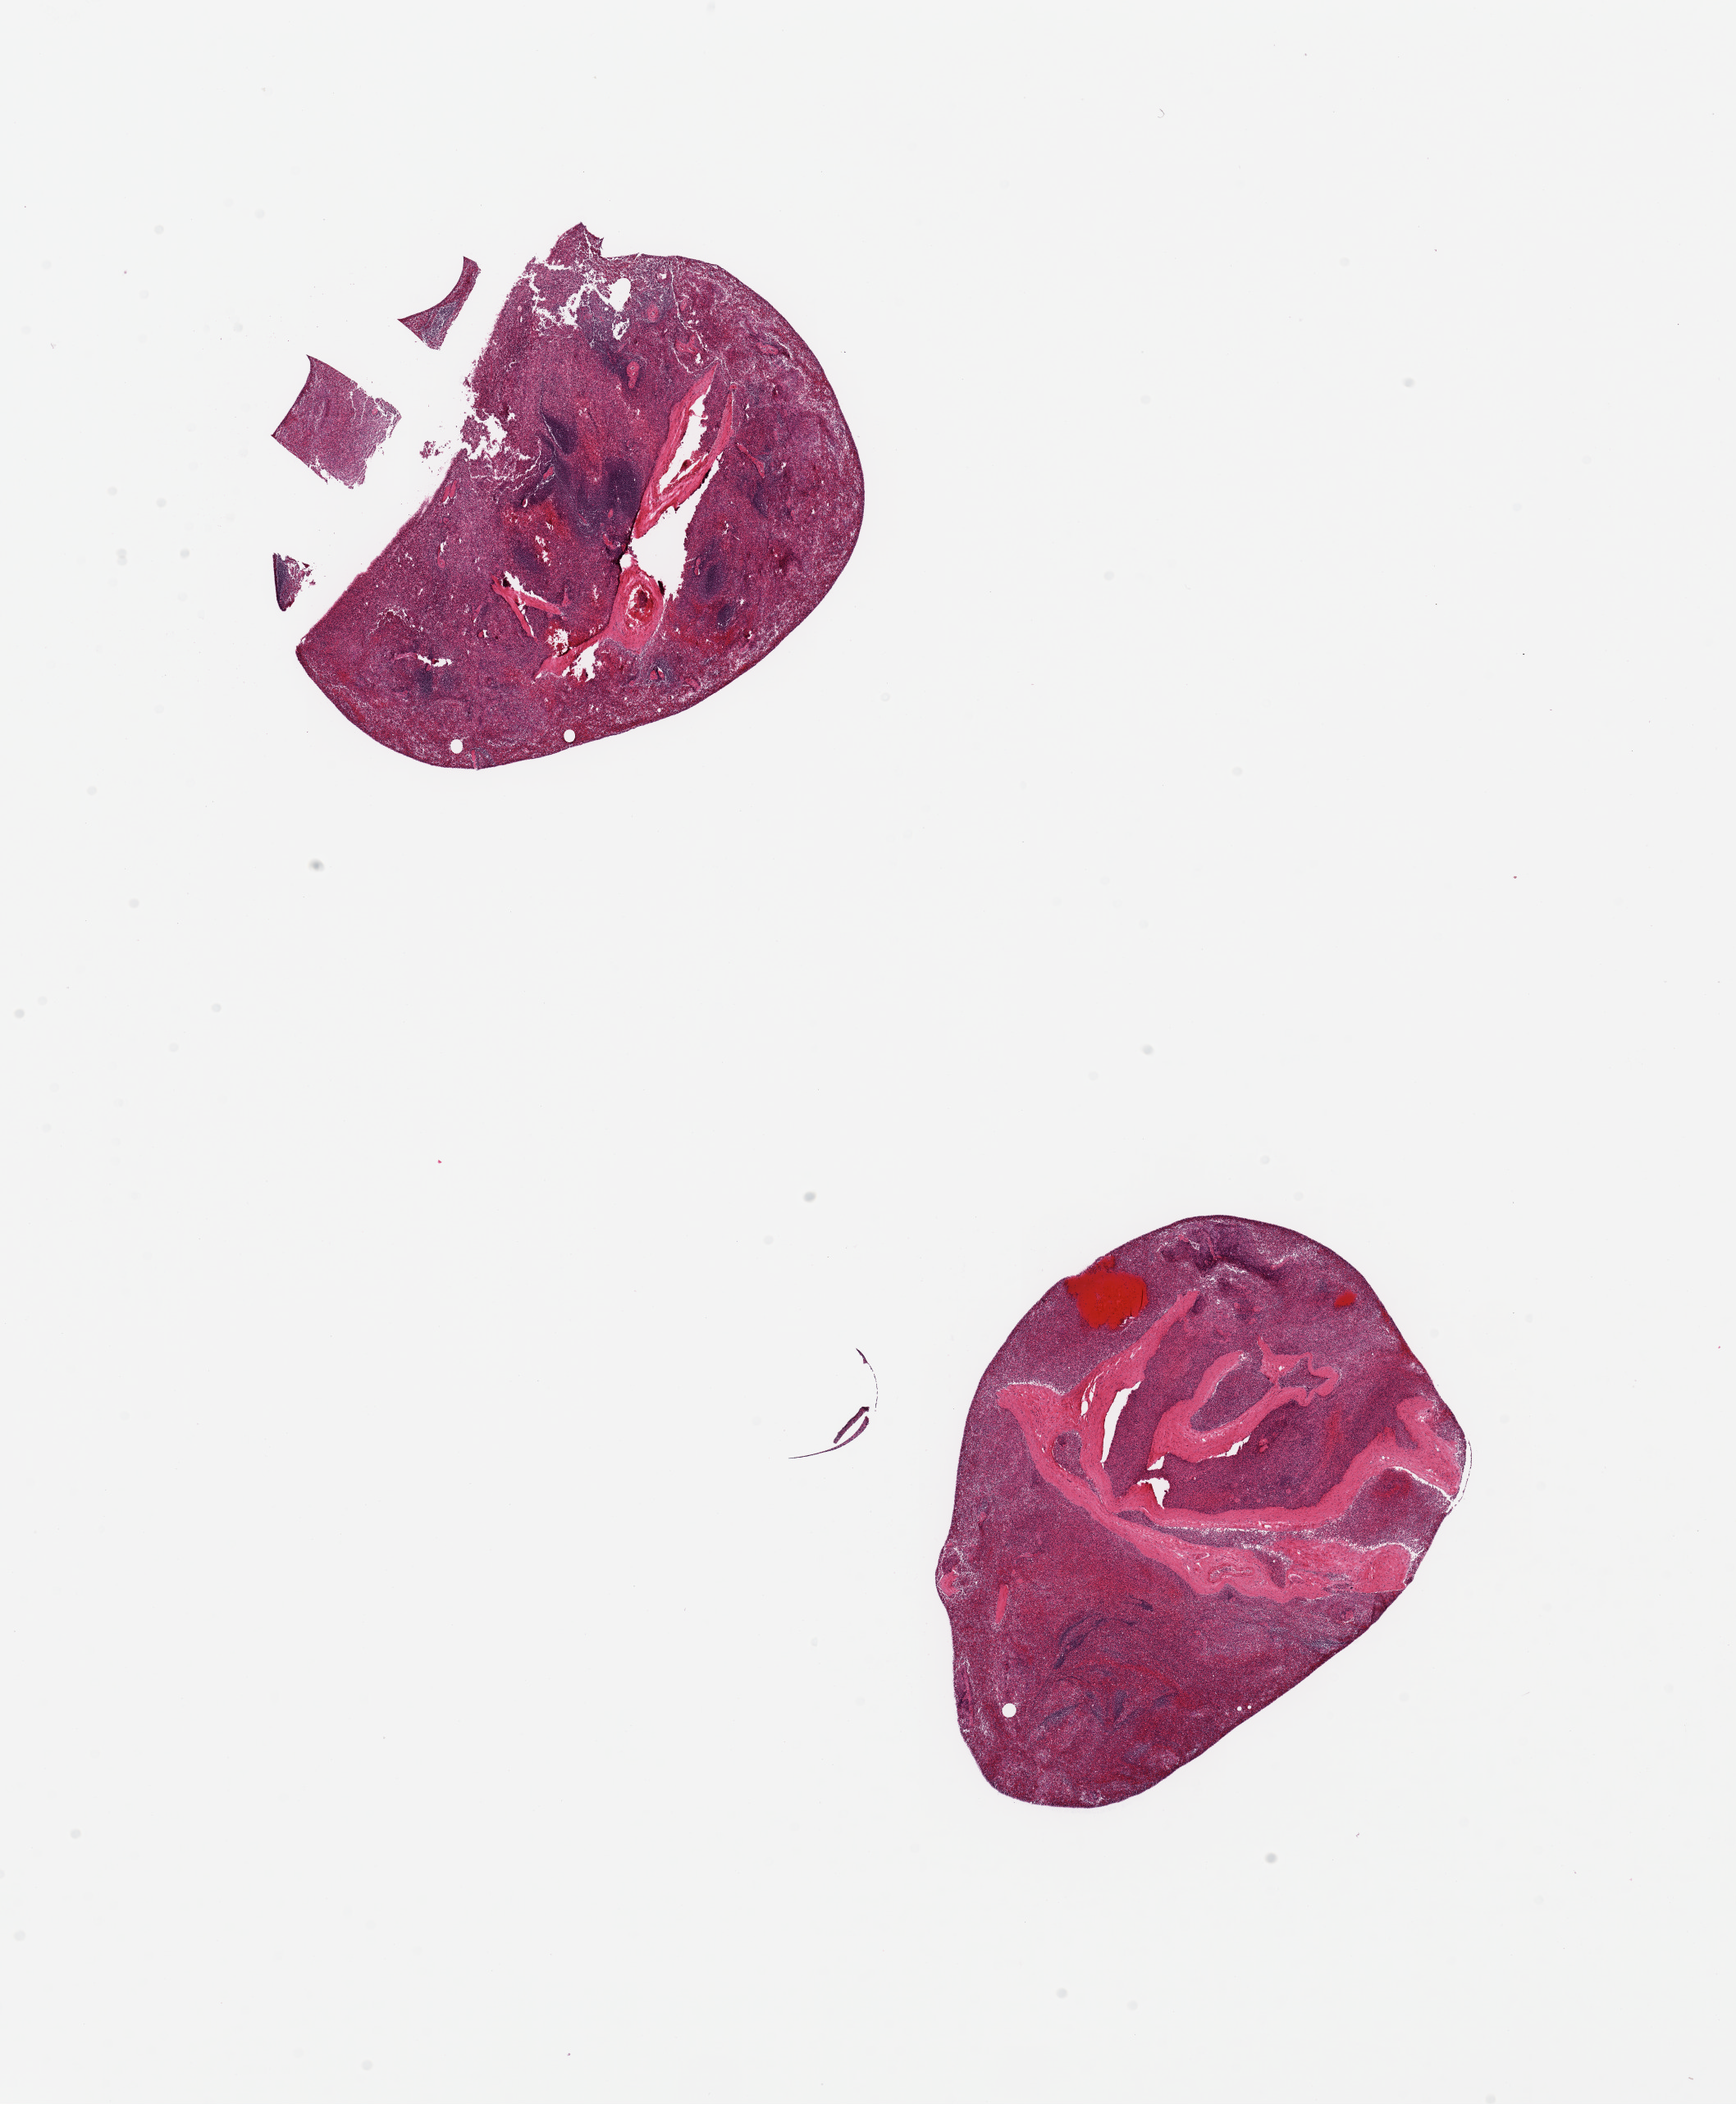
Hematoxylin and eosin (H&E) whole-slide image, brightfield — shown as a low-resolution overview of the whole scanned area (about 16.7 x 20.3 mm, acquisition: 20x scan); PAXgene-fixed, paraffin-embedded tissue; target tissue: spleen; tissue donor sample. Donor sex: female.
Pathologist's review note for this sample: 2 pieces moderate congestion.